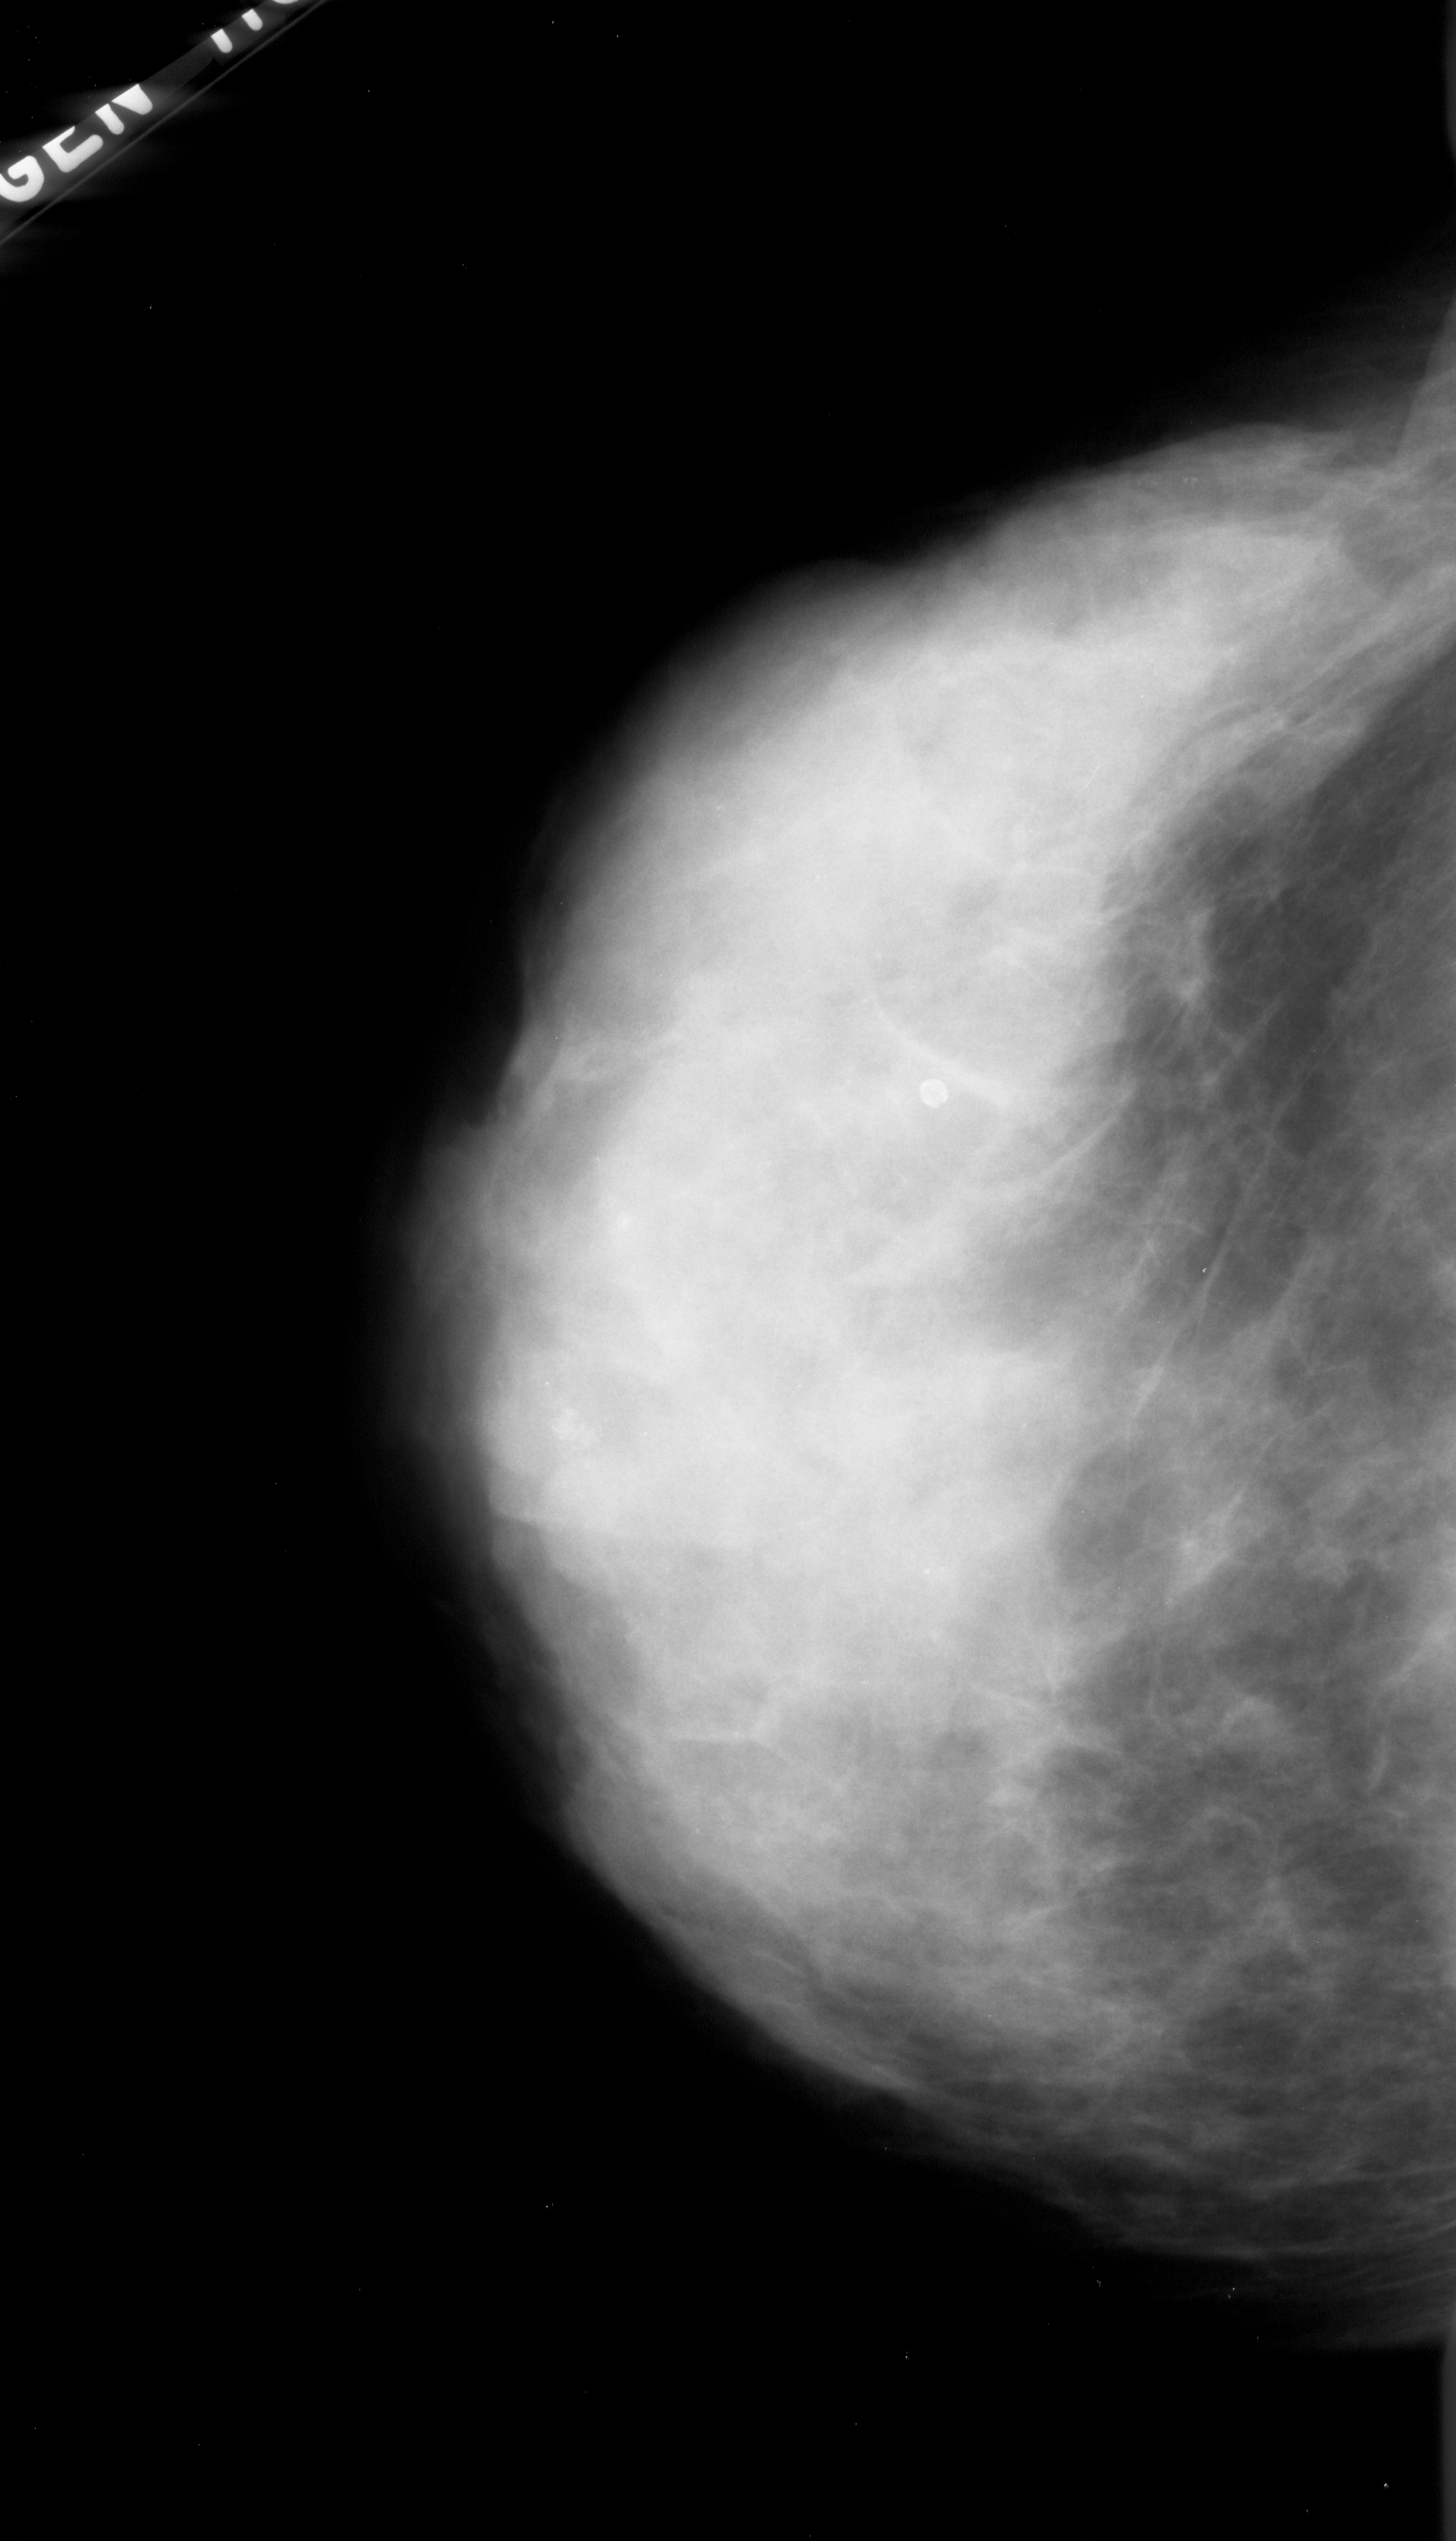
Mammogram (digitized film); left breast; craniocaudal (CC) view; BI-RADS breast density category 4 (scale 1–4); 1456 × 2541 image matrix.
Expert-marked regions of interest on this film, with their recorded descriptors:
- calcifications, morphology amorphous, distribution clustered; BI-RADS assessment category 4; subtlety rating 2 on a 1 (subtle) to 5 (obvious) scale; pathology (as recorded): malignant: bounding box [x1, y1, x2, y2] px = [537, 1390, 622, 1463]